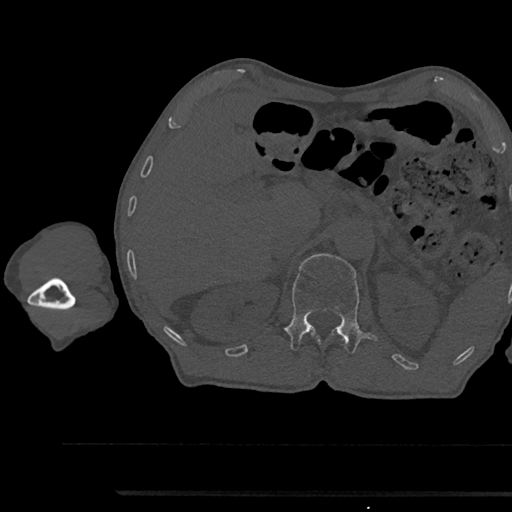
CT including the spine, one axial slice. Position 662 of 797 along the scan axis. 120 kVp. Bone window (W 1800 / L 400 HU). 0.5 mm slice thickness. 512 × 512 image matrix, field of view 367 × 367 mm. Patient: male, 79 years. From the clinical record (not read from this slice): primary cancer: prostate.
Structures marked on this image (semi-automatic segmentation, software-assisted and operator-edited):
- L1 vertebra: bounding box <284,253,378,353> (left, top, right, bottom; pixels)